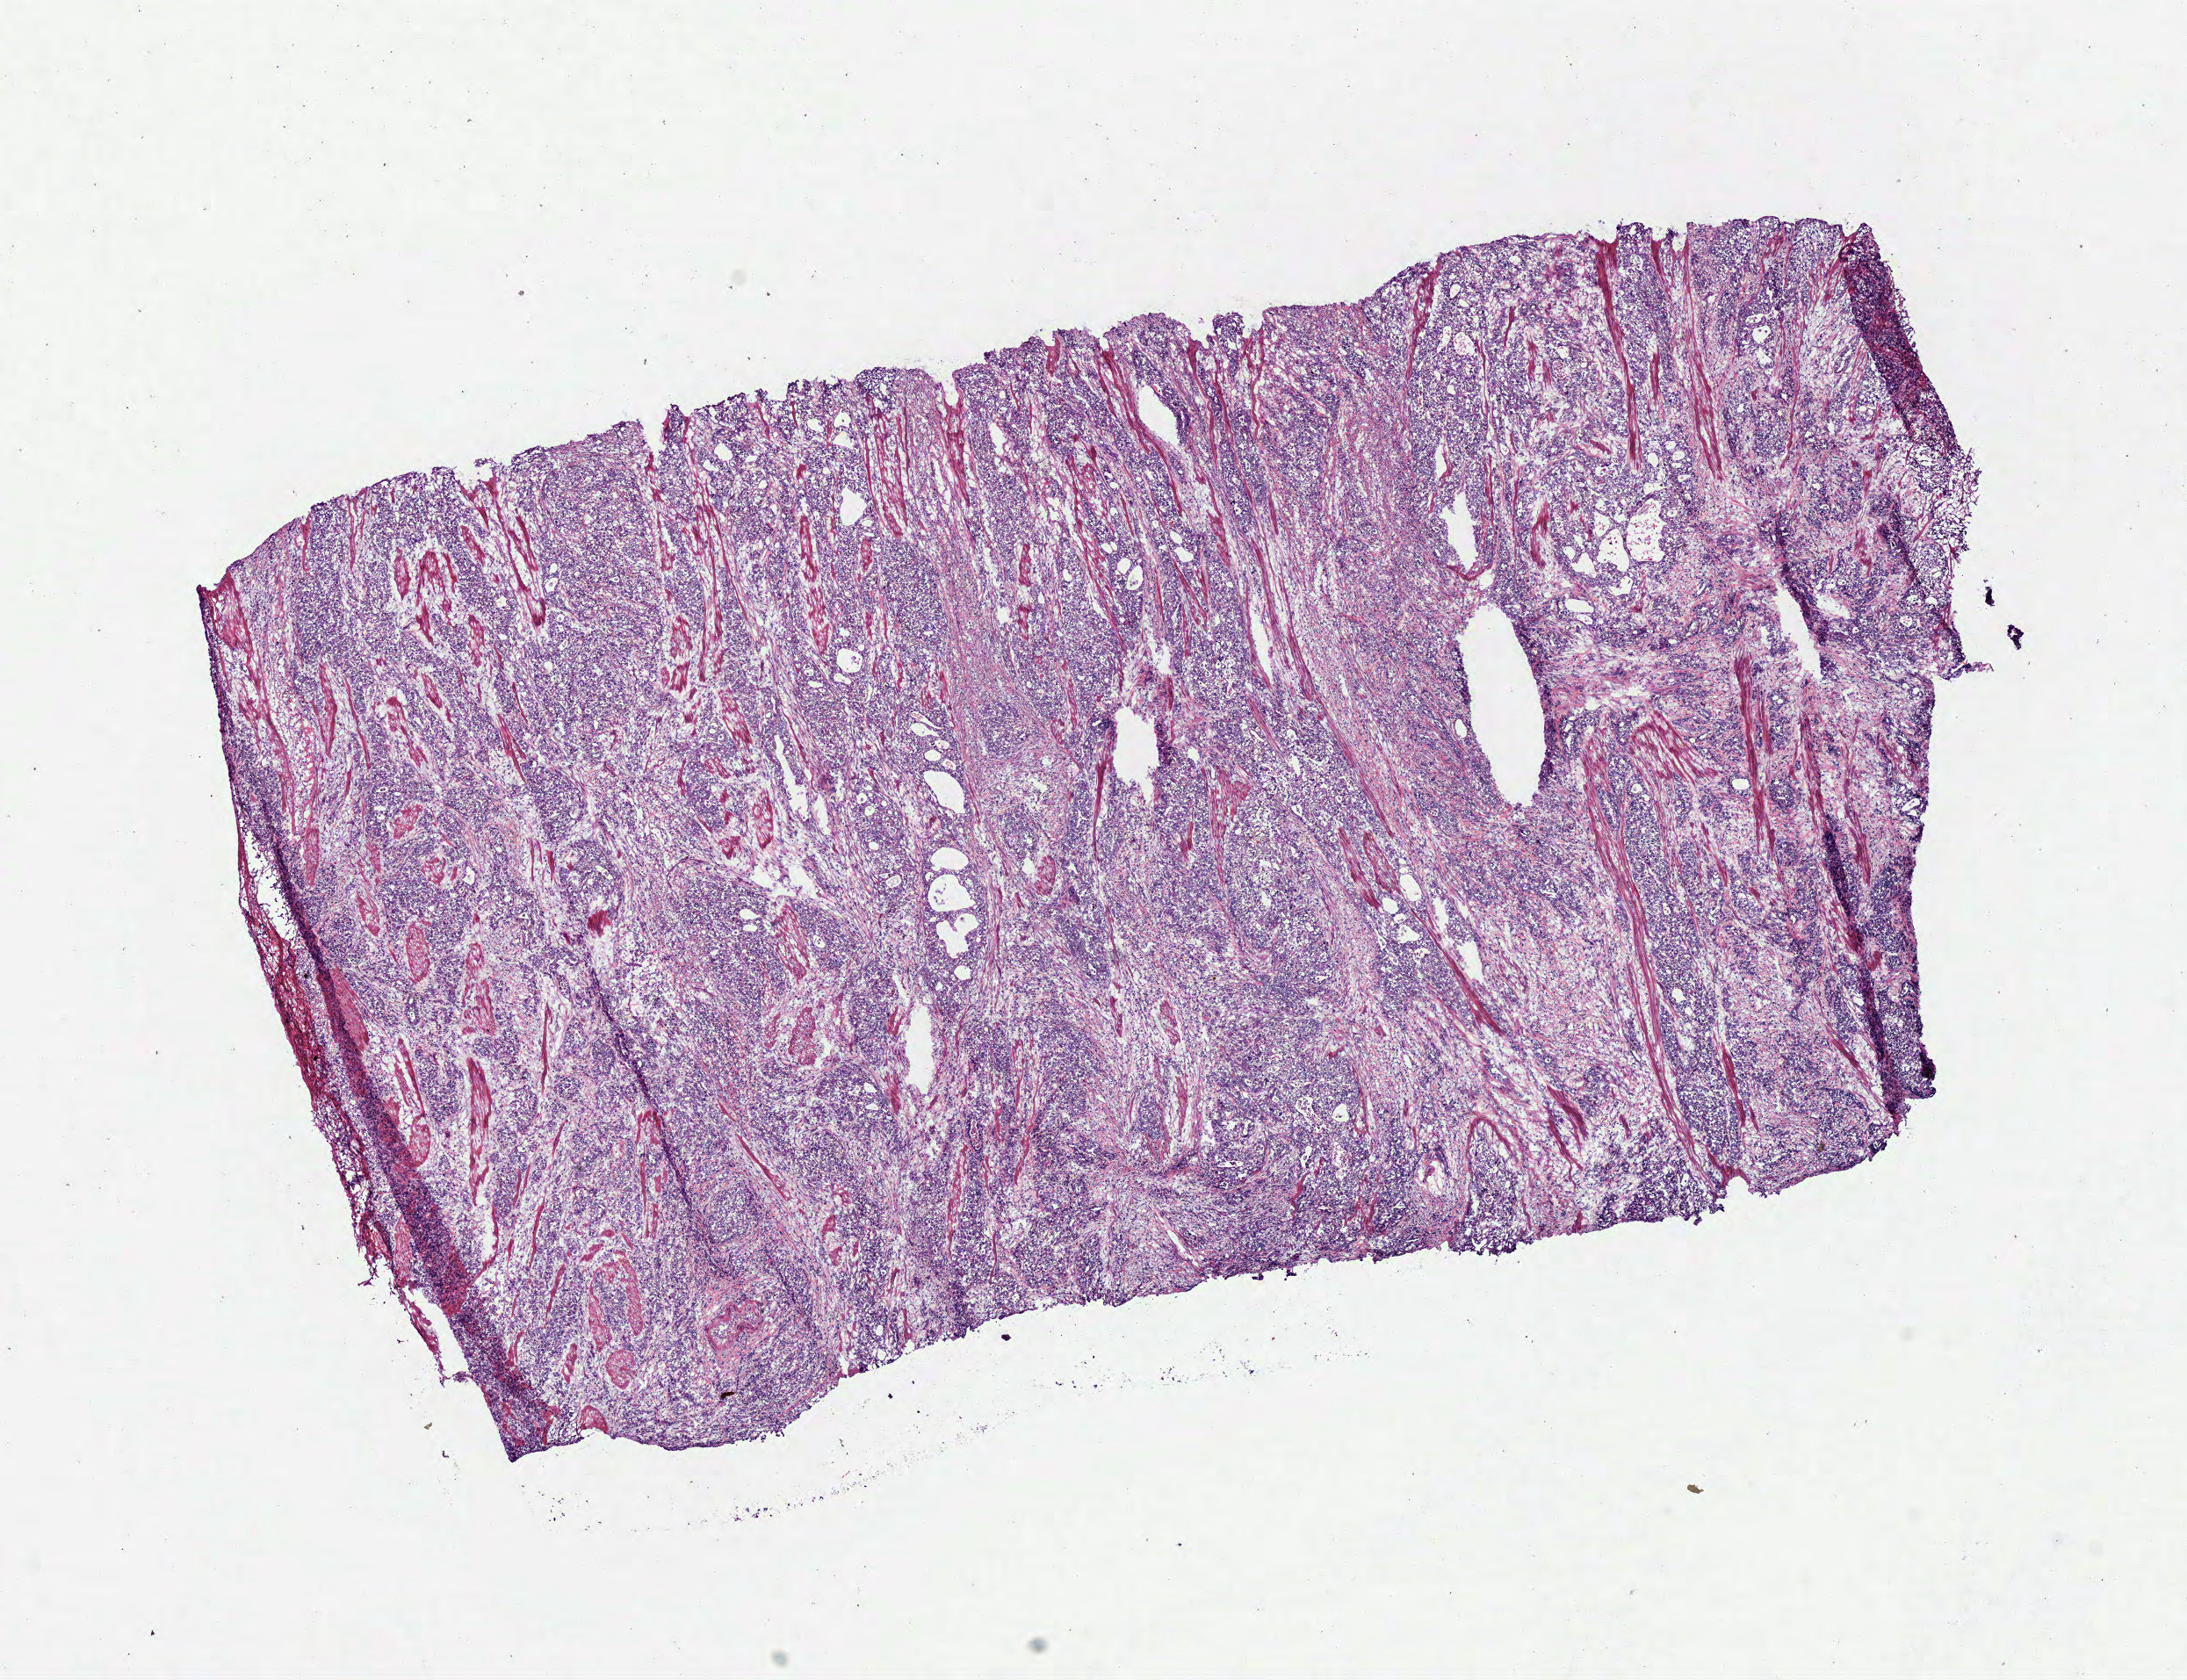
Whole-slide histology image, H&E-stained — low-resolution overview of the scanned area, about 9.8 x 7.5 mm, frozen section from the bottom of the tissue portion, stomach, primary tumour sample. Patient: male, age at initial diagnosis 53 years. Histologic grade: G3 (poorly differentiated). Pathologist review of this section (percent, as recorded): tumour cells 85%, tumour nuclei 85%, normal cells 0%, stromal cells 15%, necrosis 0%.
AJCC pathologic stage: IIIA (6th edition). Lymph nodes positive (case pathology): 14 of 24 examined. Diagnosis: Tubular adenocarcinoma.